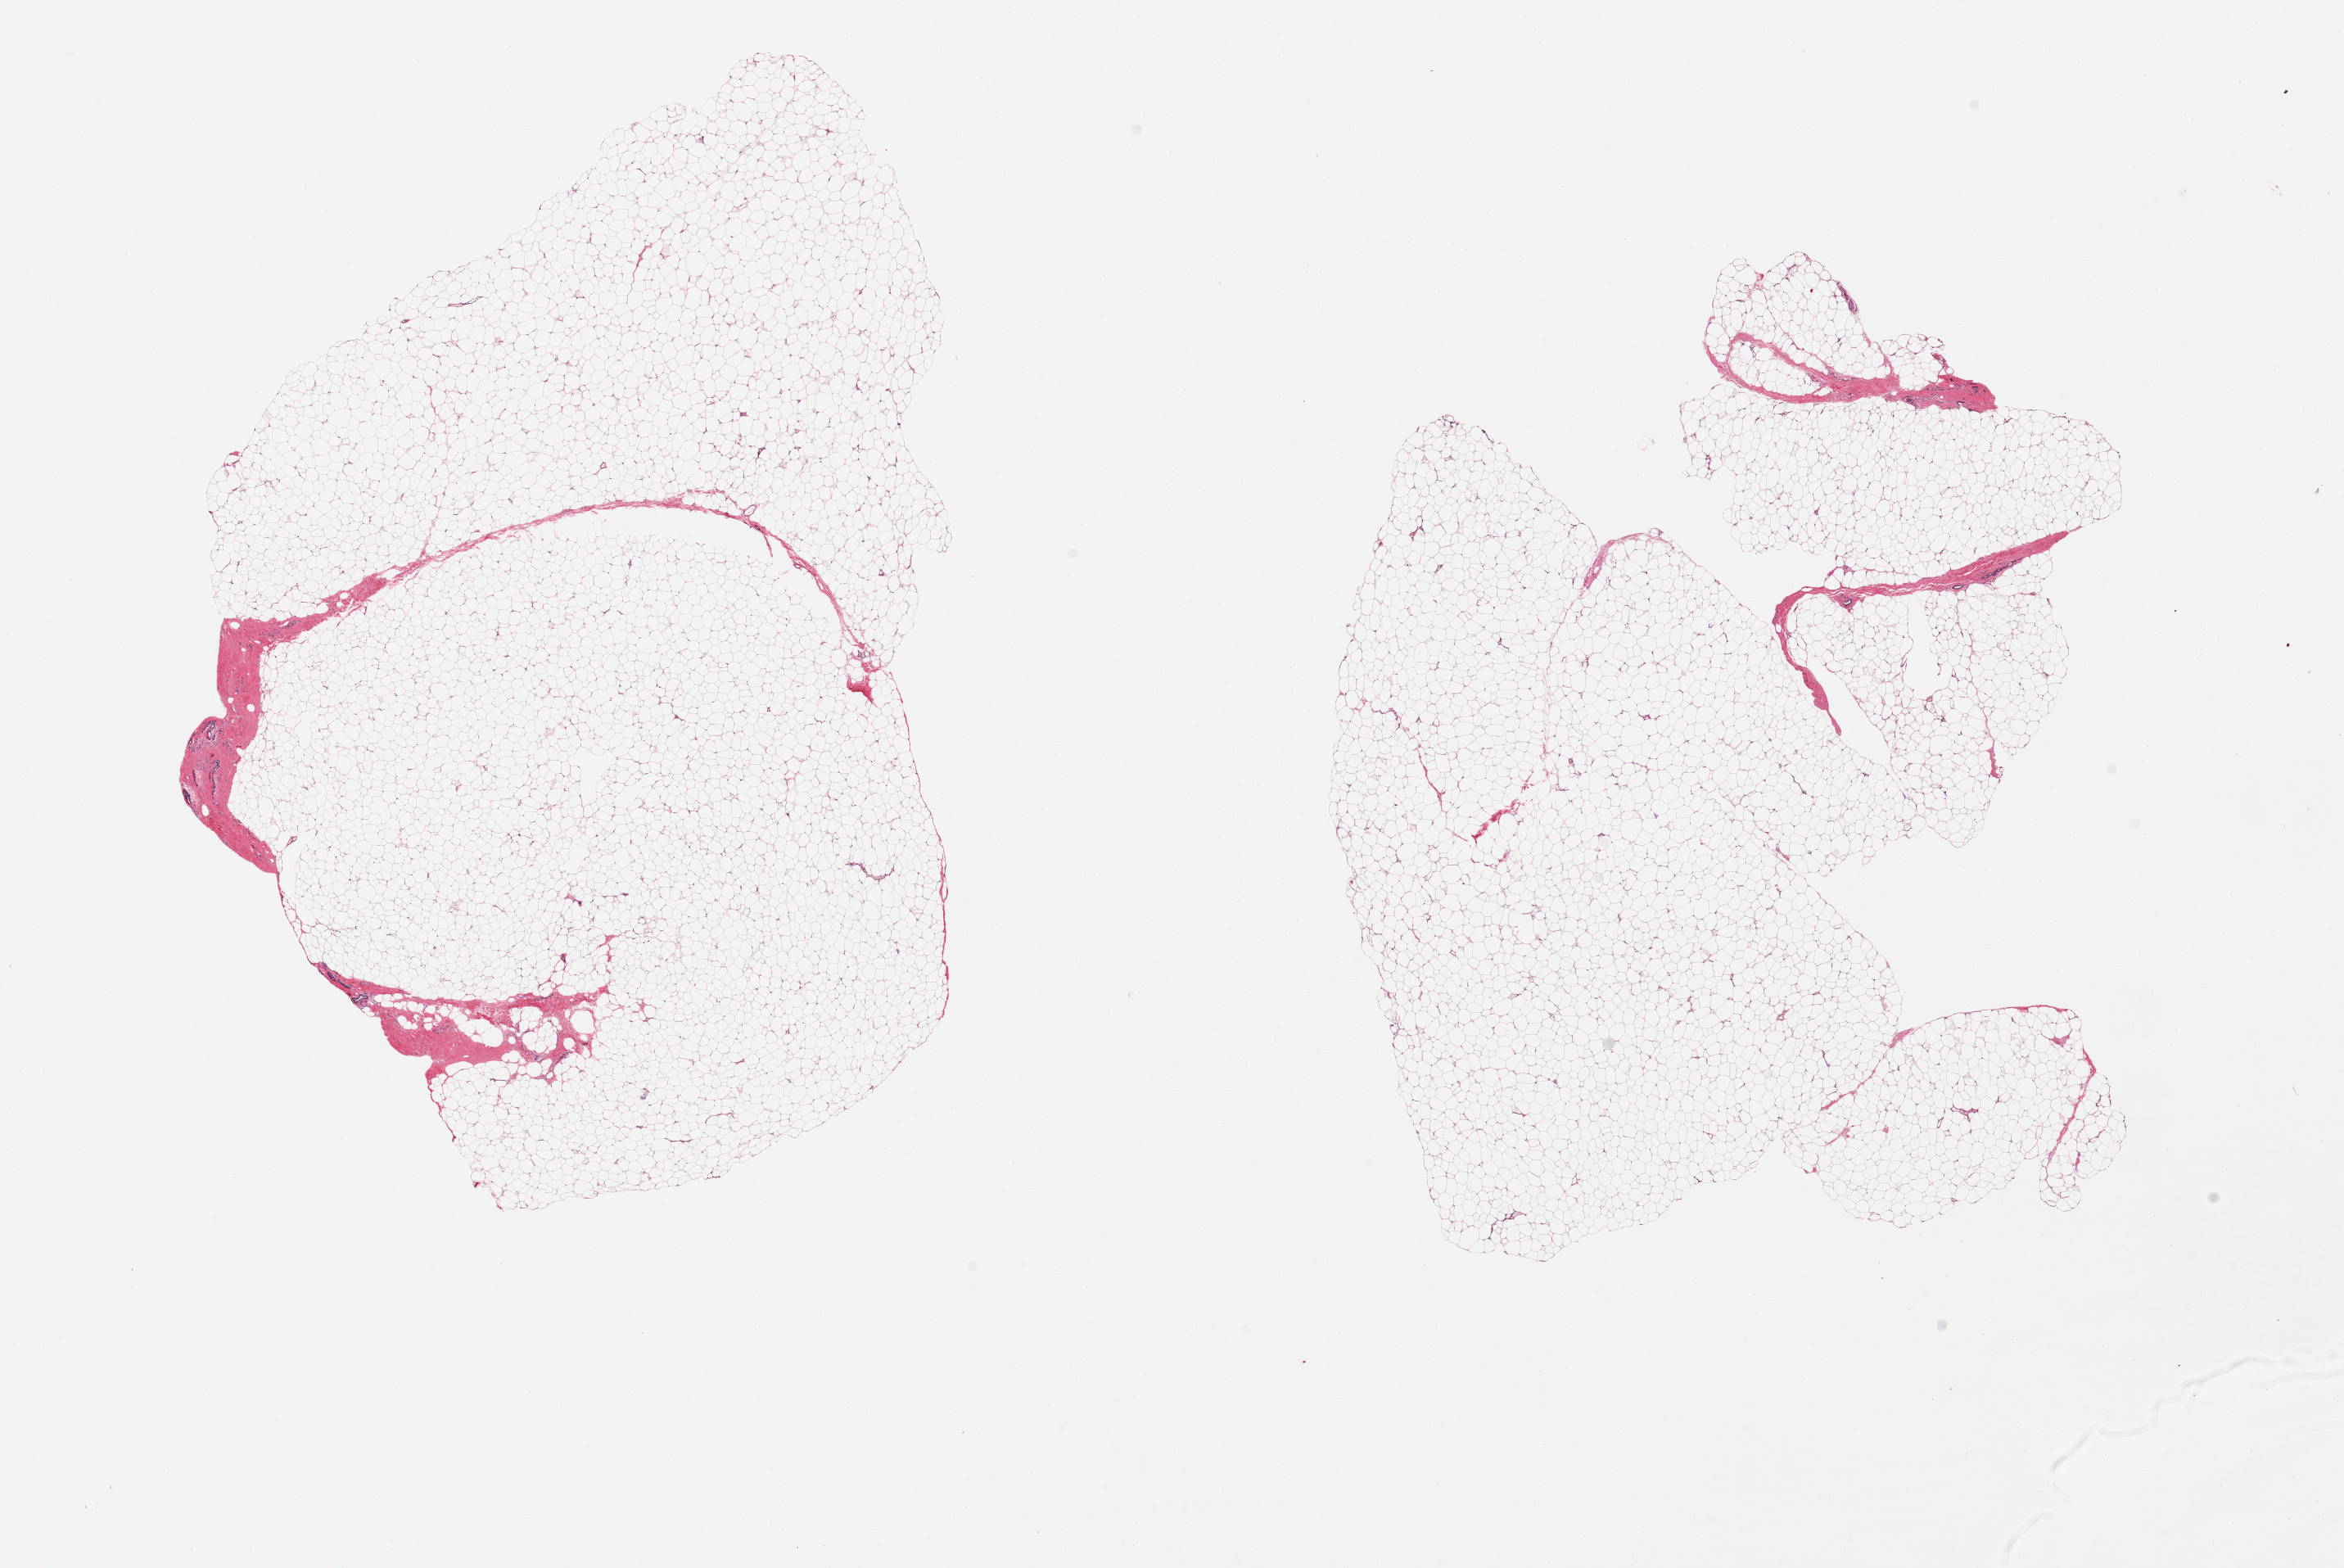
Digitized hematoxylin and eosin (H&E)-stained section — low-resolution overview of the scanned area, about 22.6 x 15.1 mm (from a 20x scan); PAXgene-fixed paraffin-embedded (PFPE) section; target tissue: breast; tissue donor sample. Donor sex: male.
* pathologist's review note for this sample: 2 pieces; predominantly fat with minimal fibrocollagenous stroma and few ducts